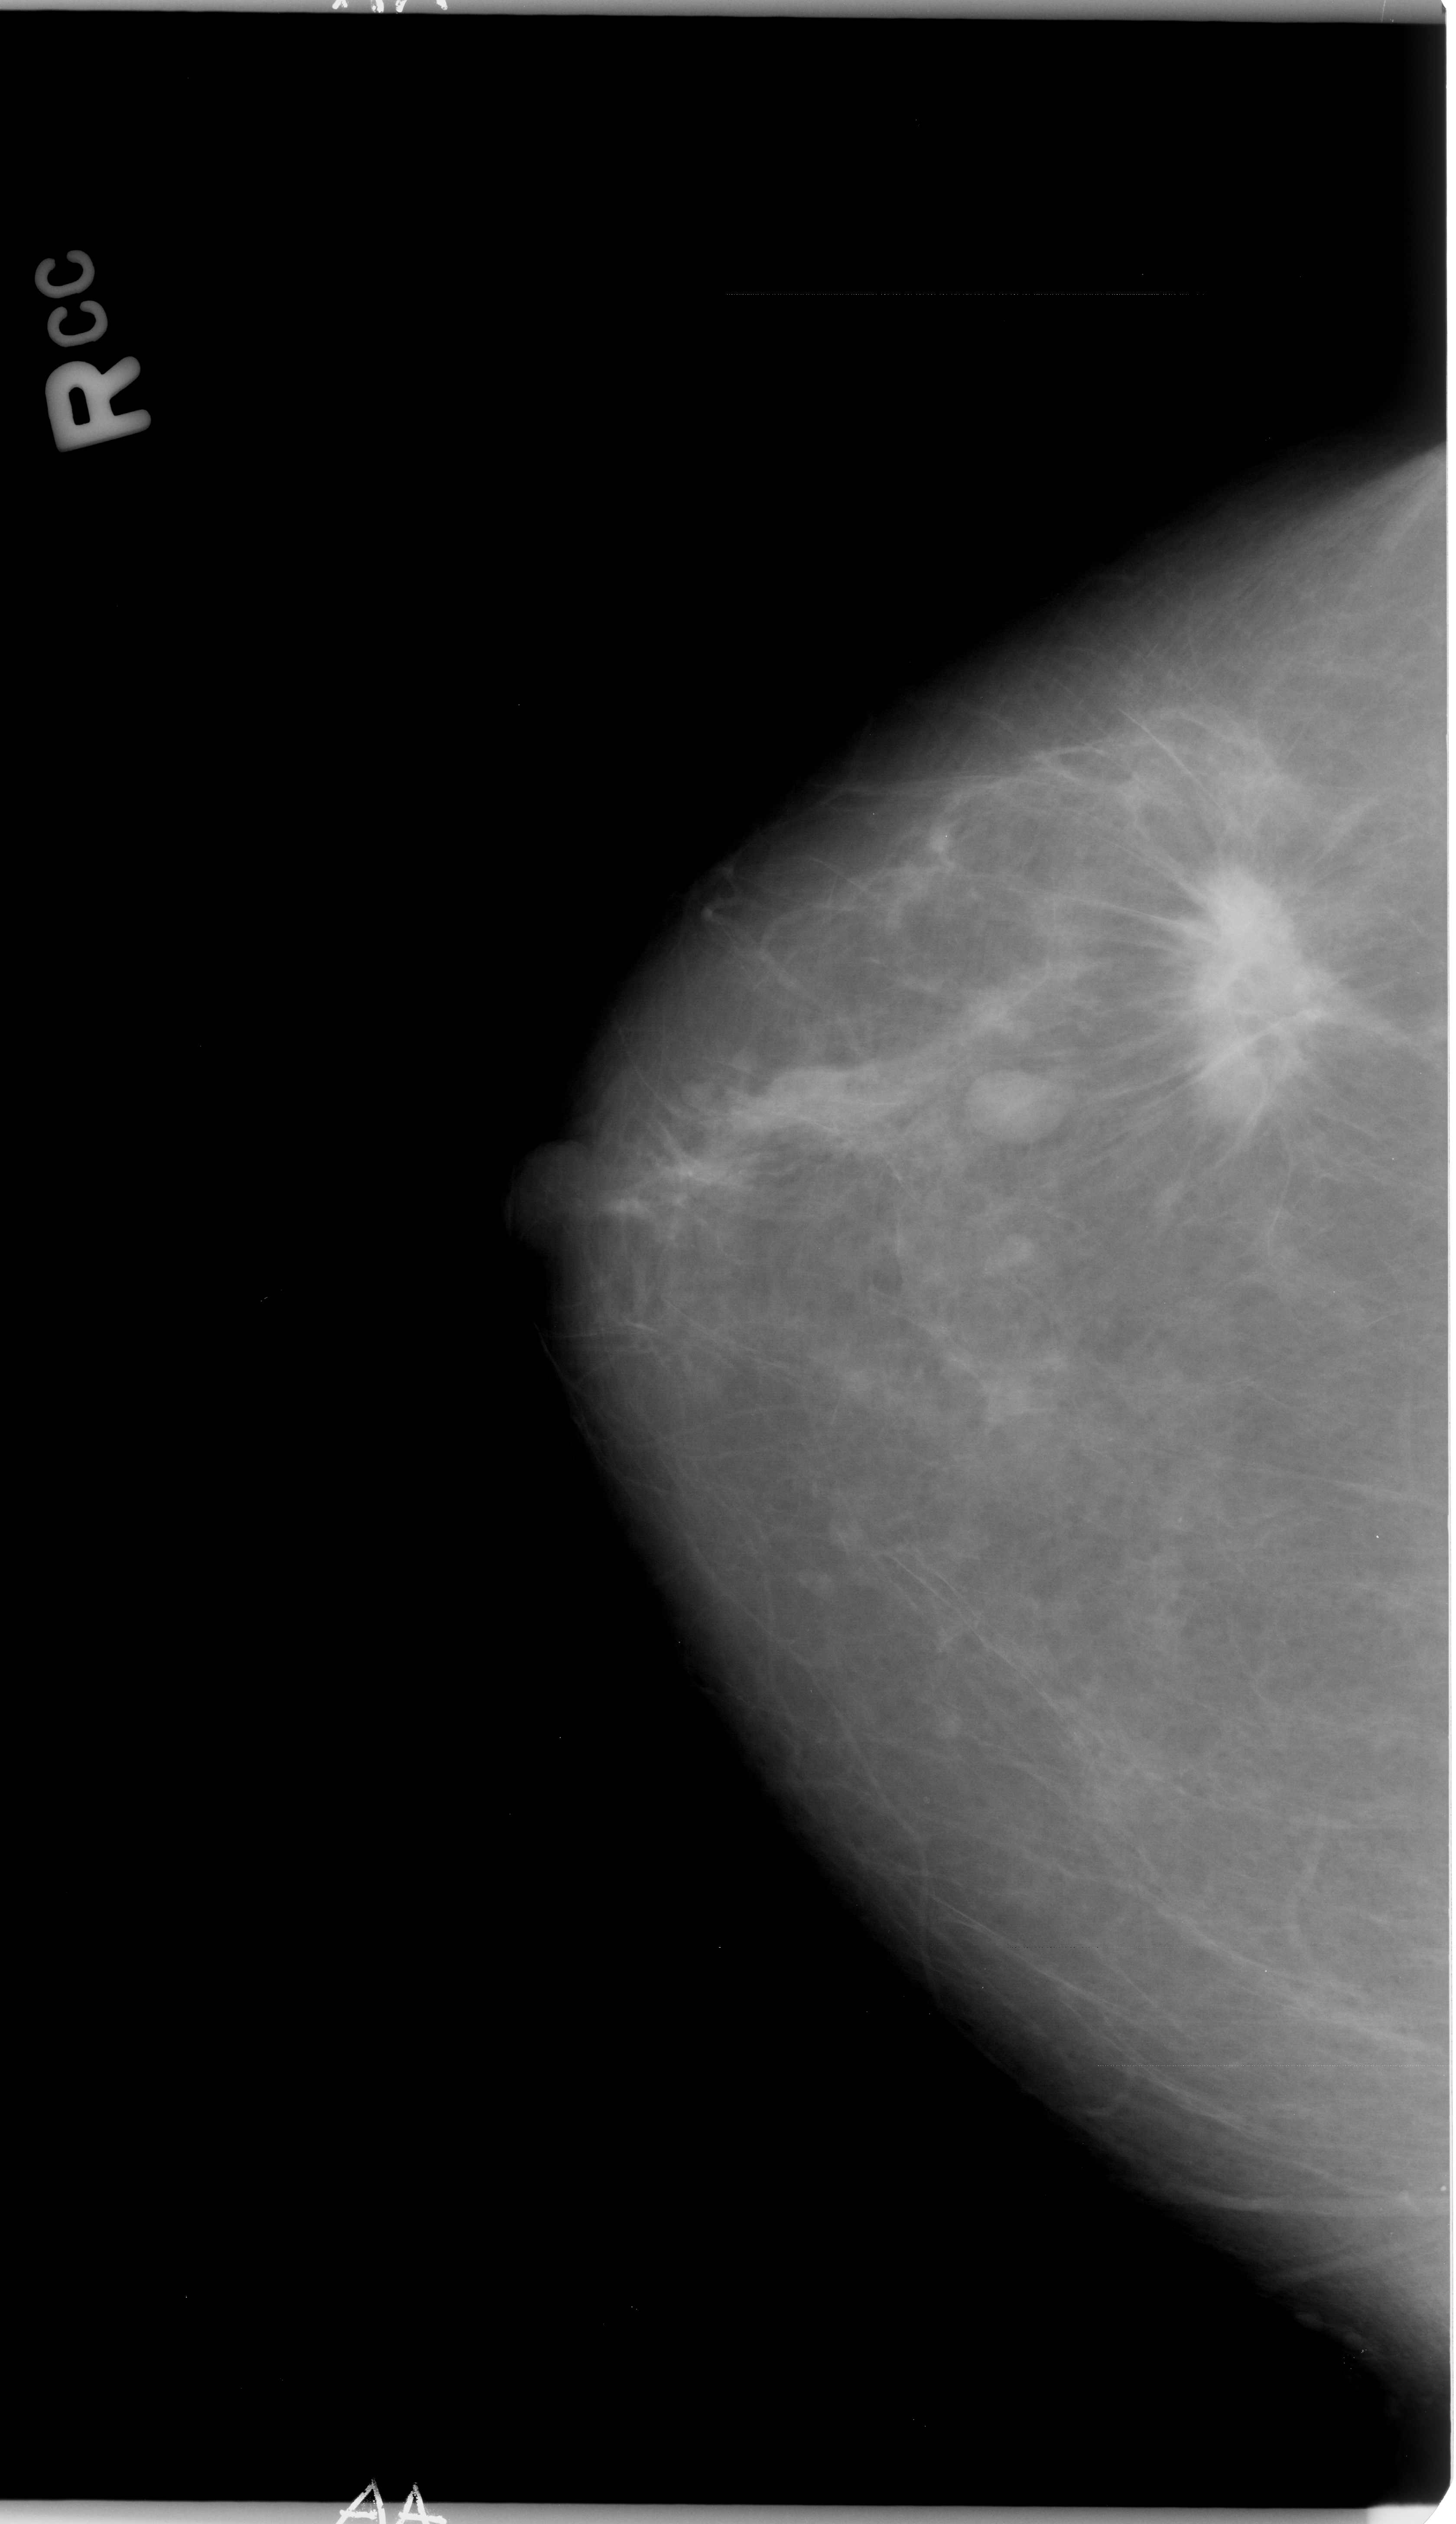
Scanned film-screen mammogram, right breast, craniocaudal (CC) view, BI-RADS breast density category 2 (scale 1–4).
Finding: mass, shape irregular / architectural distortion, margins spiculated; BI-RADS assessment category 5; pathology result (as recorded, not read from the image): malignant.